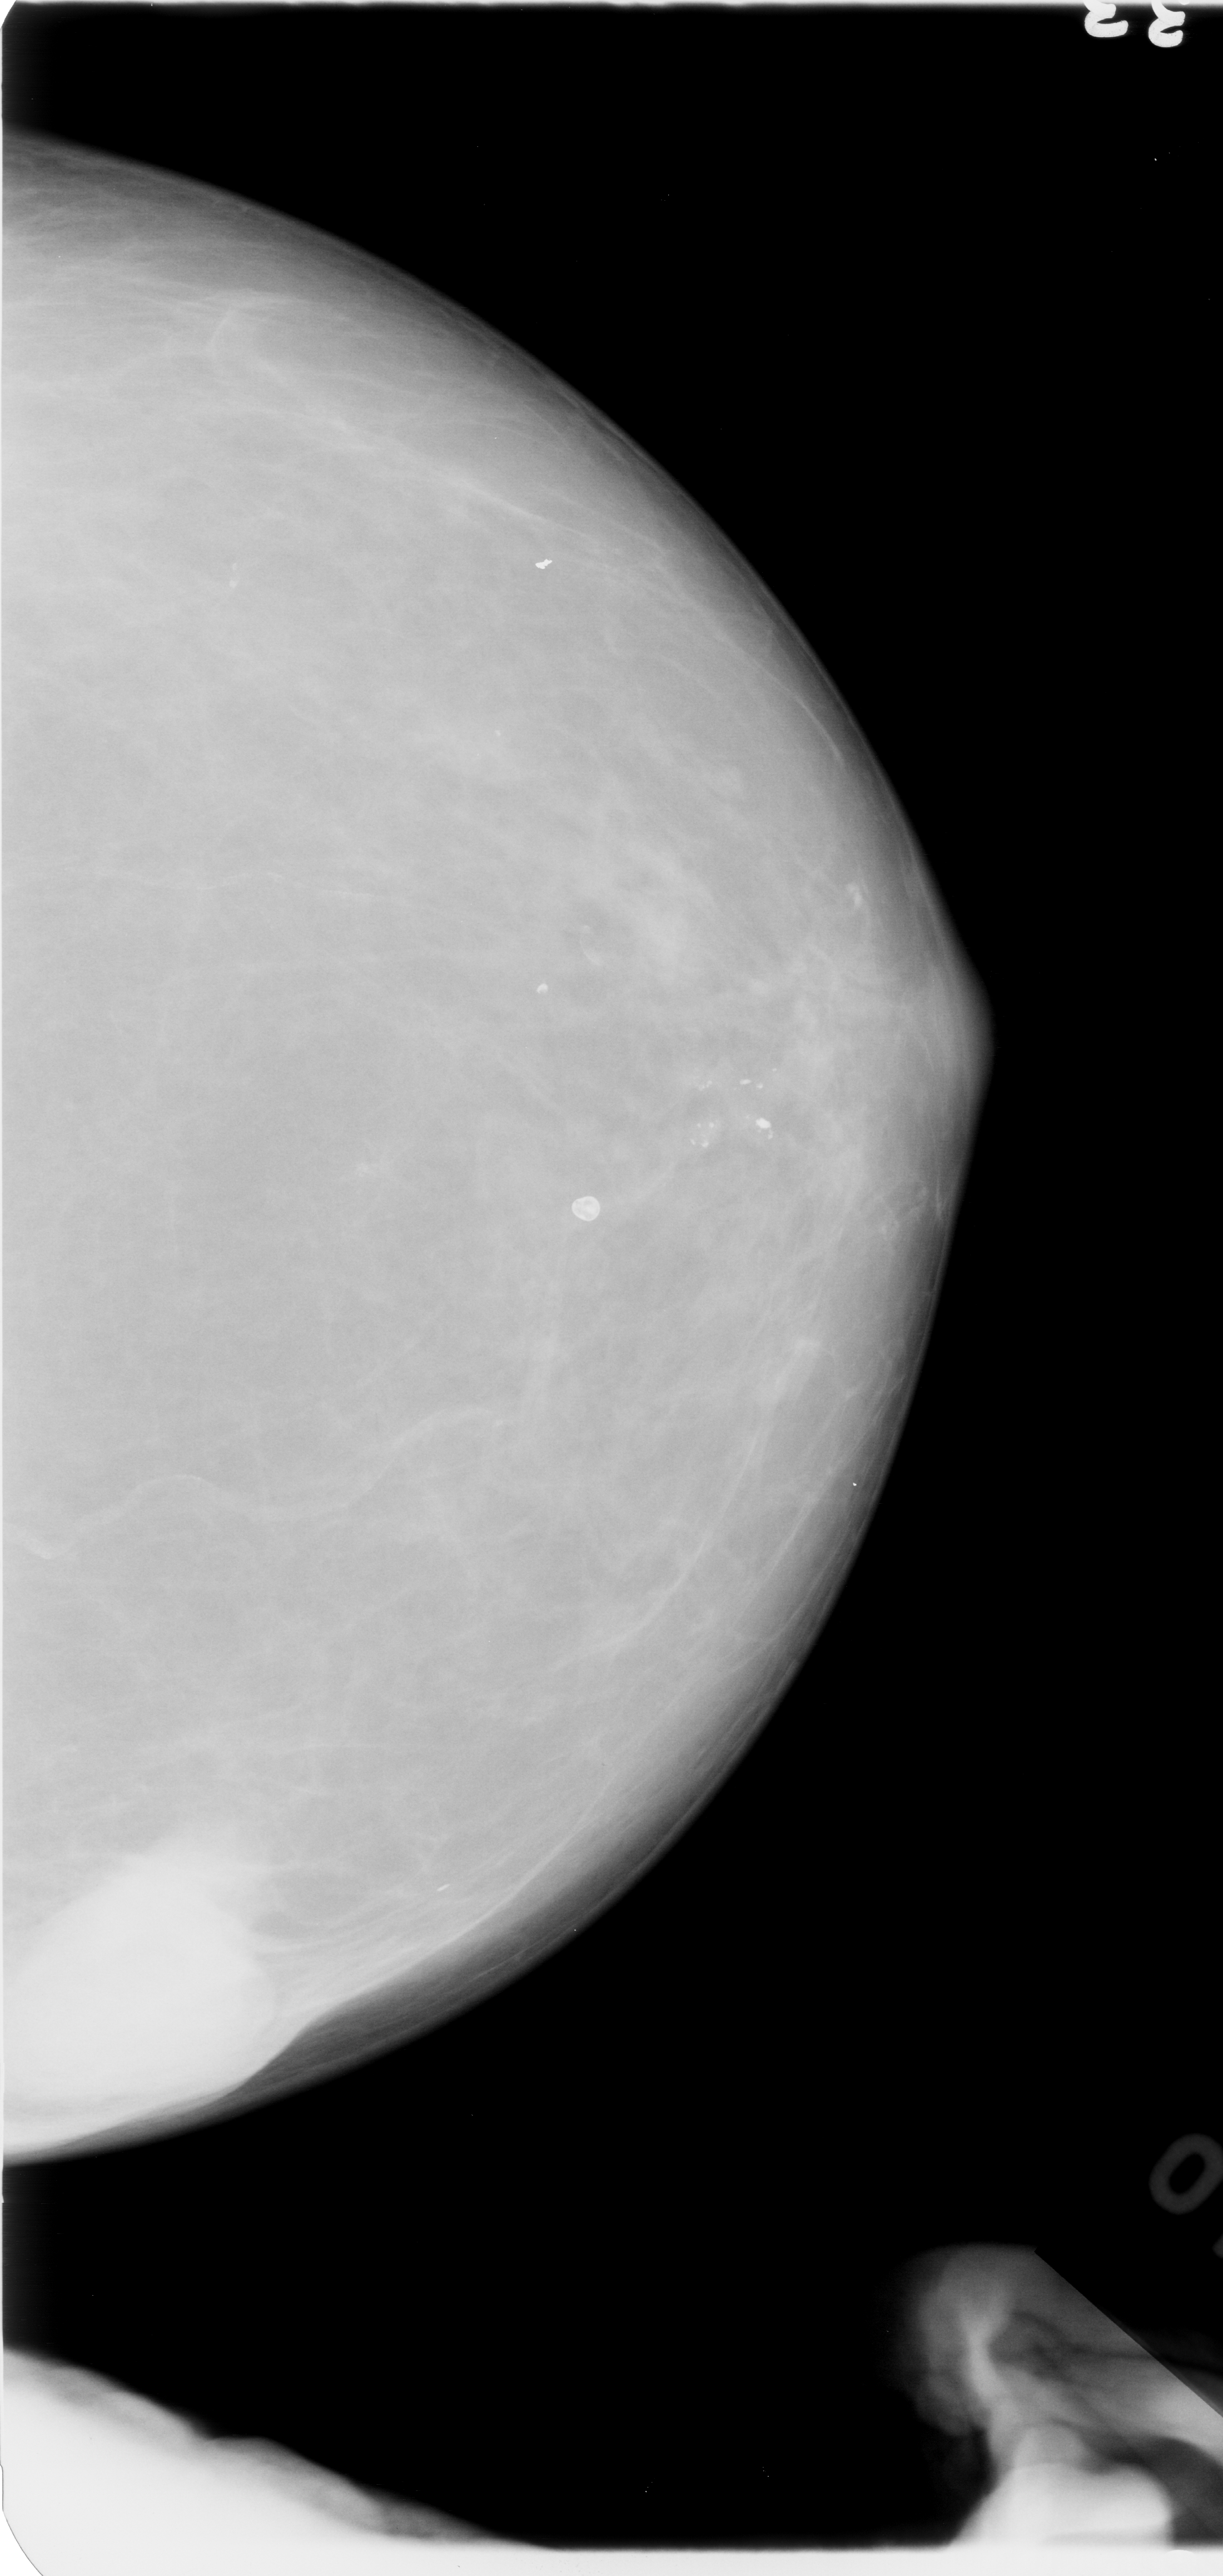
Mammogram (digitized film). Left breast. Craniocaudal (CC) view. BI-RADS breast density category 1 (scale 1–4). 1223 × 2576 image matrix.
Expert-marked regions of interest on this image (one box per marked abnormality):
- mass, shape irregular, margins circumscribed / ill defined; BI-RADS assessment category 4; pathology result (as recorded, not read from the image): malignant: box from (x=3, y=1854) to (x=271, y=2134) px